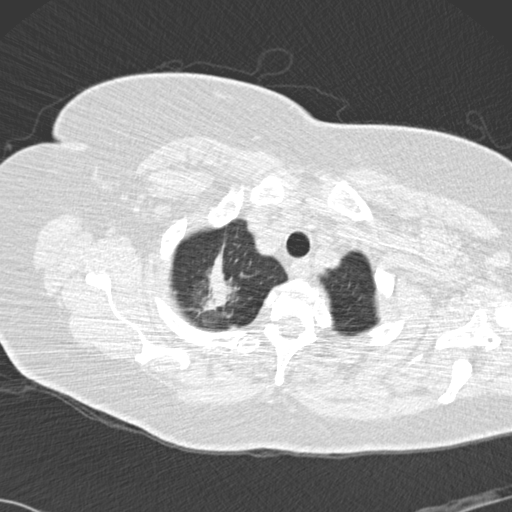
Low-dose screening chest CT, one axial slice. Slice 130 of 146 in the series (ordered by position). Reconstruction kernel B30f. 120 kVp. Lung window (W 1500 / L -600 HU). 2 mm slice thickness. 512 × 512 image matrix, field of view 350 × 350 mm.
Outlined on this slice (expert manual segmentation):
- lesion 1 (tumor, upper lobe of right lung): bounding box <201,246,237,312> (left, top, right, bottom; pixels)